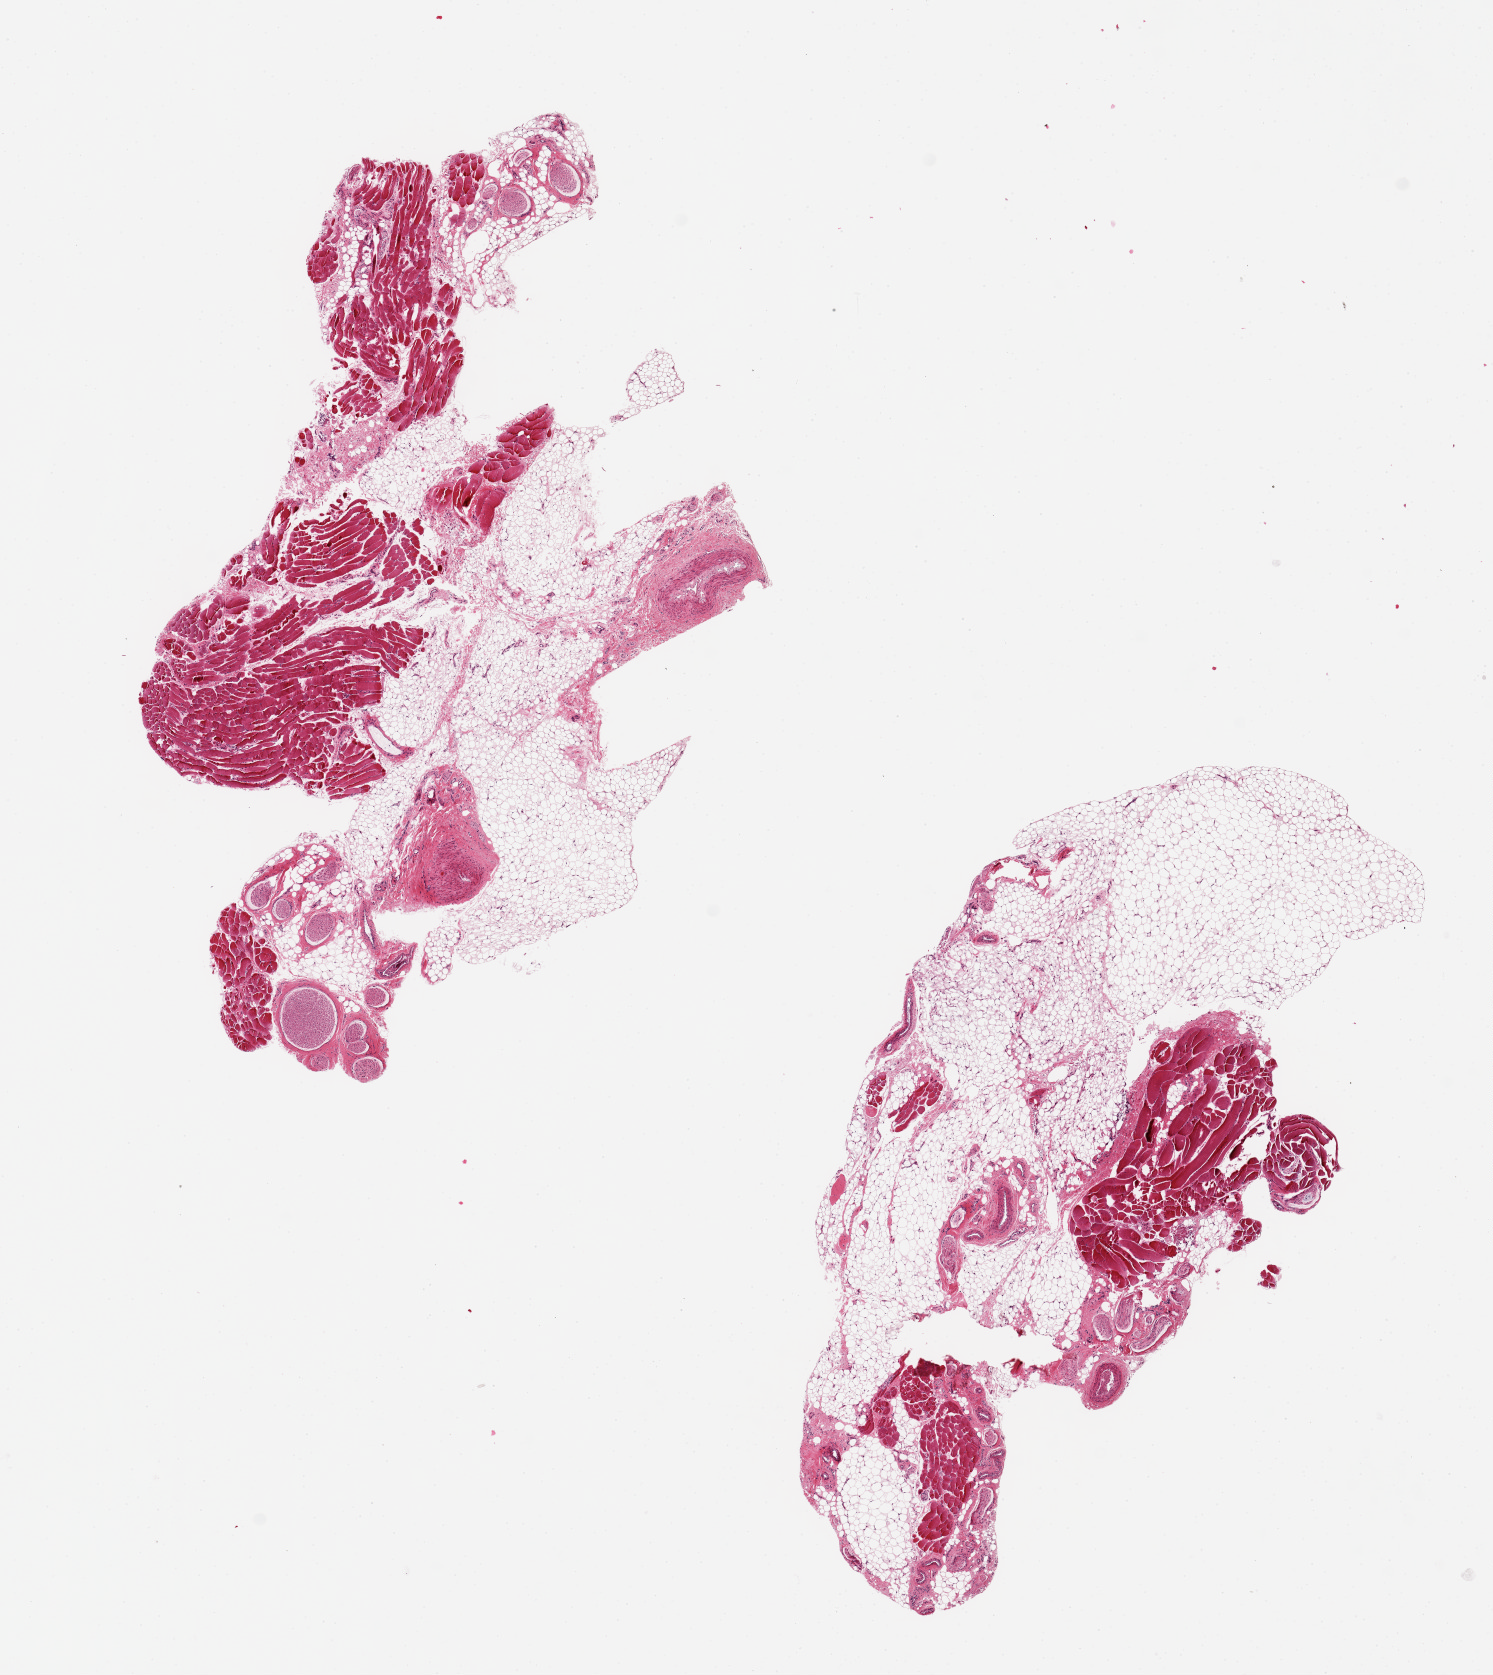
Whole-slide image, hematoxylin and eosin (H&E) stain — a low-resolution overview of the entire scanned area, about 11.8 x 13.3 mm, PAXgene-fixed, paraffin-embedded tissue, section of minor salivary gland (target tissue), tissue donor sample. Donor: male.
• review note (as recorded): 2 pieces, 8x5 & 7x4mm; No salivary glands; all muscle, nerve, adipose